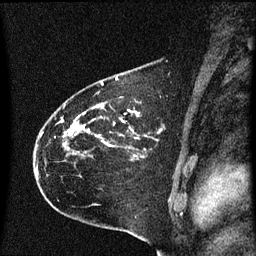
Breast MRI (dynamic contrast-enhanced), one sagittal slice; position 44 of 60 along the scan axis; dynamic contrast-enhanced series, image 2 of 3 at this slice position (ordered by acquisition); 1.5 T; TE 4.2 ms, TR 8.4 ms; 2 mm slice thickness; 256 × 256 image matrix, field of view 200 × 200 mm. Female patient, age 35 years. Case-level facts recorded for this patient, not image findings: setting: breast cancer imaged before/during neoadjuvant chemotherapy; receptor status: HER2-positive.
Outlined on this slice (semi-automatically segmented with operator editing):
- analysis volume of interest (the breast-tissue region the enhancement analysis was run in; not a lesion): bounding box <36,68,166,173> (left, top, right, bottom; pixels)
- tumour enhancement mask (voxels above the 70 % enhancement threshold inside the analysis volume of interest): <67,78,139,137>